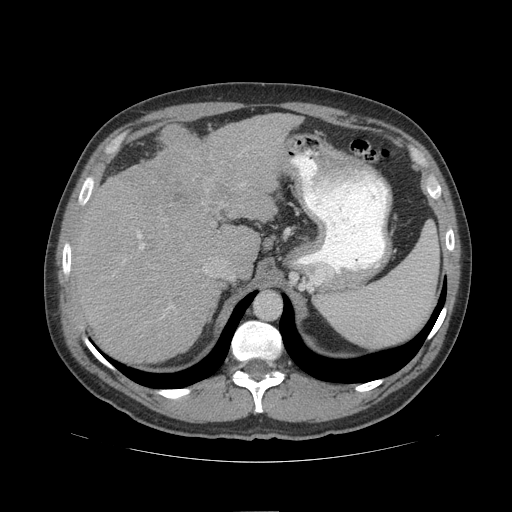
Contrast-enhanced abdominal CT (liver protocol), one axial slice; position 73 of 109 along the scan axis; soft-tissue window (W 400 / L 40 HU); 2.5 mm slice thickness; 512 × 512 image matrix, field of view 420 × 420 mm. Case-level facts recorded for this patient, not image findings: diagnosis: hepatocellular carcinoma (patient treated with transarterial chemoembolisation; whether this scan precedes or follows treatment is not stated here); TNM stage (as recorded): Stage-IIIB; Child-Pugh class: A; tumour differentiation: poorly differentiated; tumour nodularity: multinodular.
Structures marked on this image (semi-automatic segmentation, software-assisted and operator-edited):
- liver parenchyma outside the tumour (the mass and vessels are separate outlines, so this box may not span the whole liver): bounding box [x1, y1, x2, y2] px = [72, 112, 300, 362]
- mass: [140, 126, 234, 208]
- liver vessels: [137, 232, 143, 249]